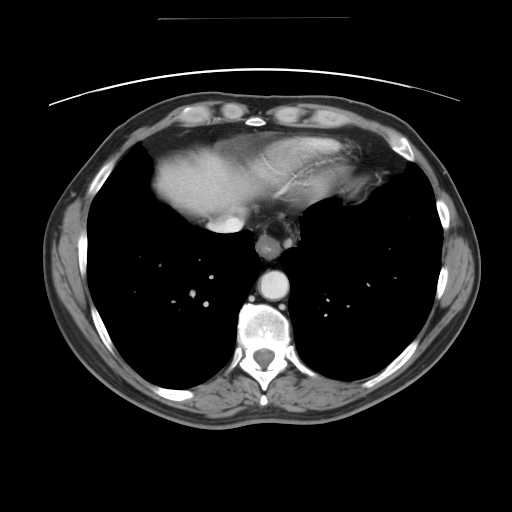
Contrast-enhanced abdominal CT, one axial slice; position 45 of 49 along the scan axis; intravenous contrast given; soft-tissue window (W 400 / L 40 HU); 5 mm slice thickness; 512 × 512 image matrix. Male patient, age 57 years. From the clinical record (not read from this slice): diagnosis: colorectal cancer liver metastases, imaged before liver resection; multiple liver metastases: yes; largest metastasis: 4 cm; disease in both lobes: no.
Outlined on this slice (outlined manually by an expert reader):
- liver: bounding box (x1, y1, x2, y2) in pixels: (153, 149, 265, 217)
- planned liver remnant (the part of the liver to remain after resection): (206, 150, 264, 214)